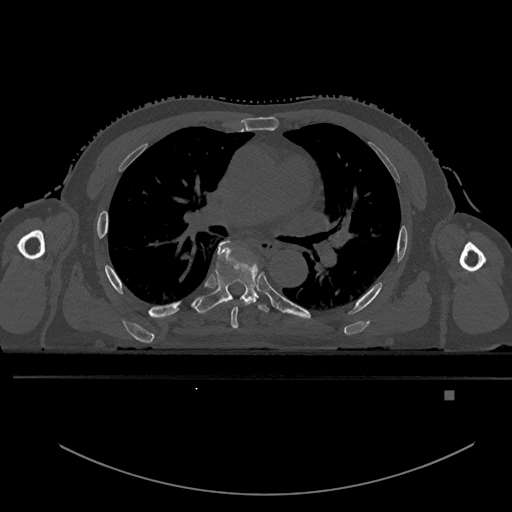
CT including the spine, one axial slice. Position 326 of 969 along the scan axis. Bone window (W 1800 / L 400 HU). 0.5 mm slice thickness. 512 × 512 image matrix, field of view 456 × 456 mm. Male patient, age 82 years. Case-level facts recorded for this patient, not image findings: primary cancer: prostate.
Annotated regions visible in this slice (semi-automatic segmentation, software-assisted and operator-edited):
- T5 vertebra: bounding box [x1, y1, x2, y2] px = [225, 240, 252, 329]
- T6 vertebra: [191, 242, 269, 314]